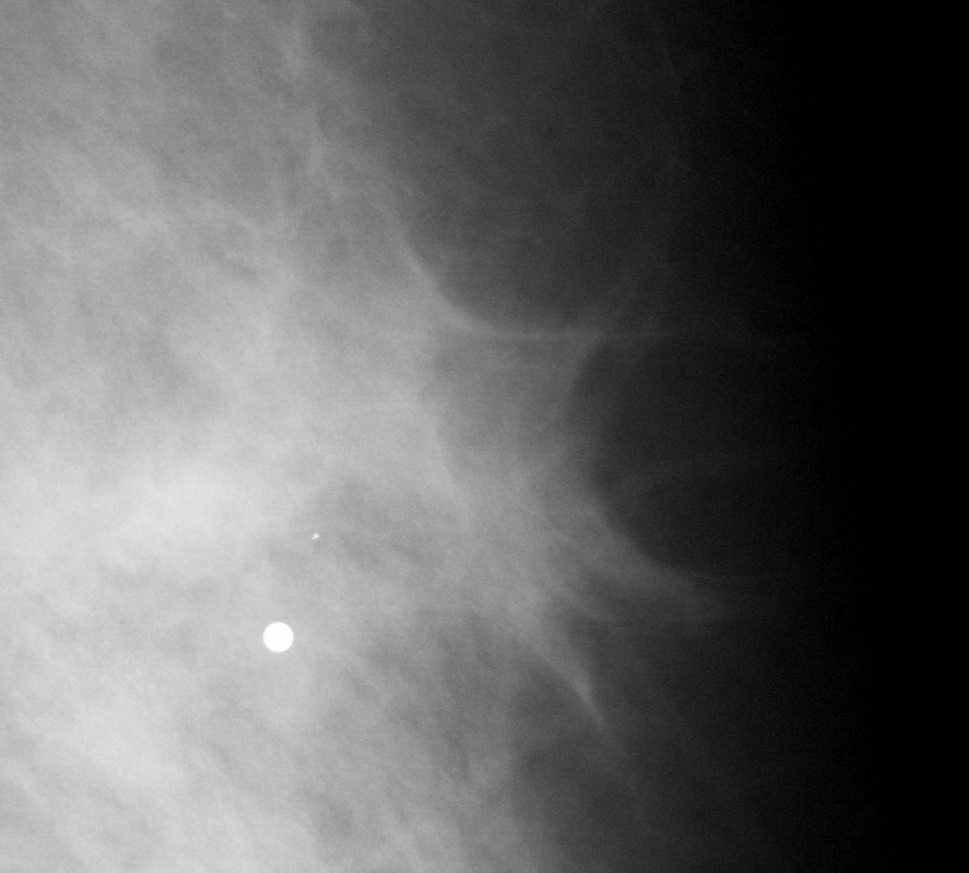
Crop from a digitized film mammogram around one marked abnormality; left breast; MLO view.
- Marked abnormality: calcifications, morphology amorphous, distribution clustered; BI-RADS assessment category 4; subtlety rating 2 on a 1 (subtle) to 5 (obvious) scale; pathology result (as recorded, not read from the image): malignant.